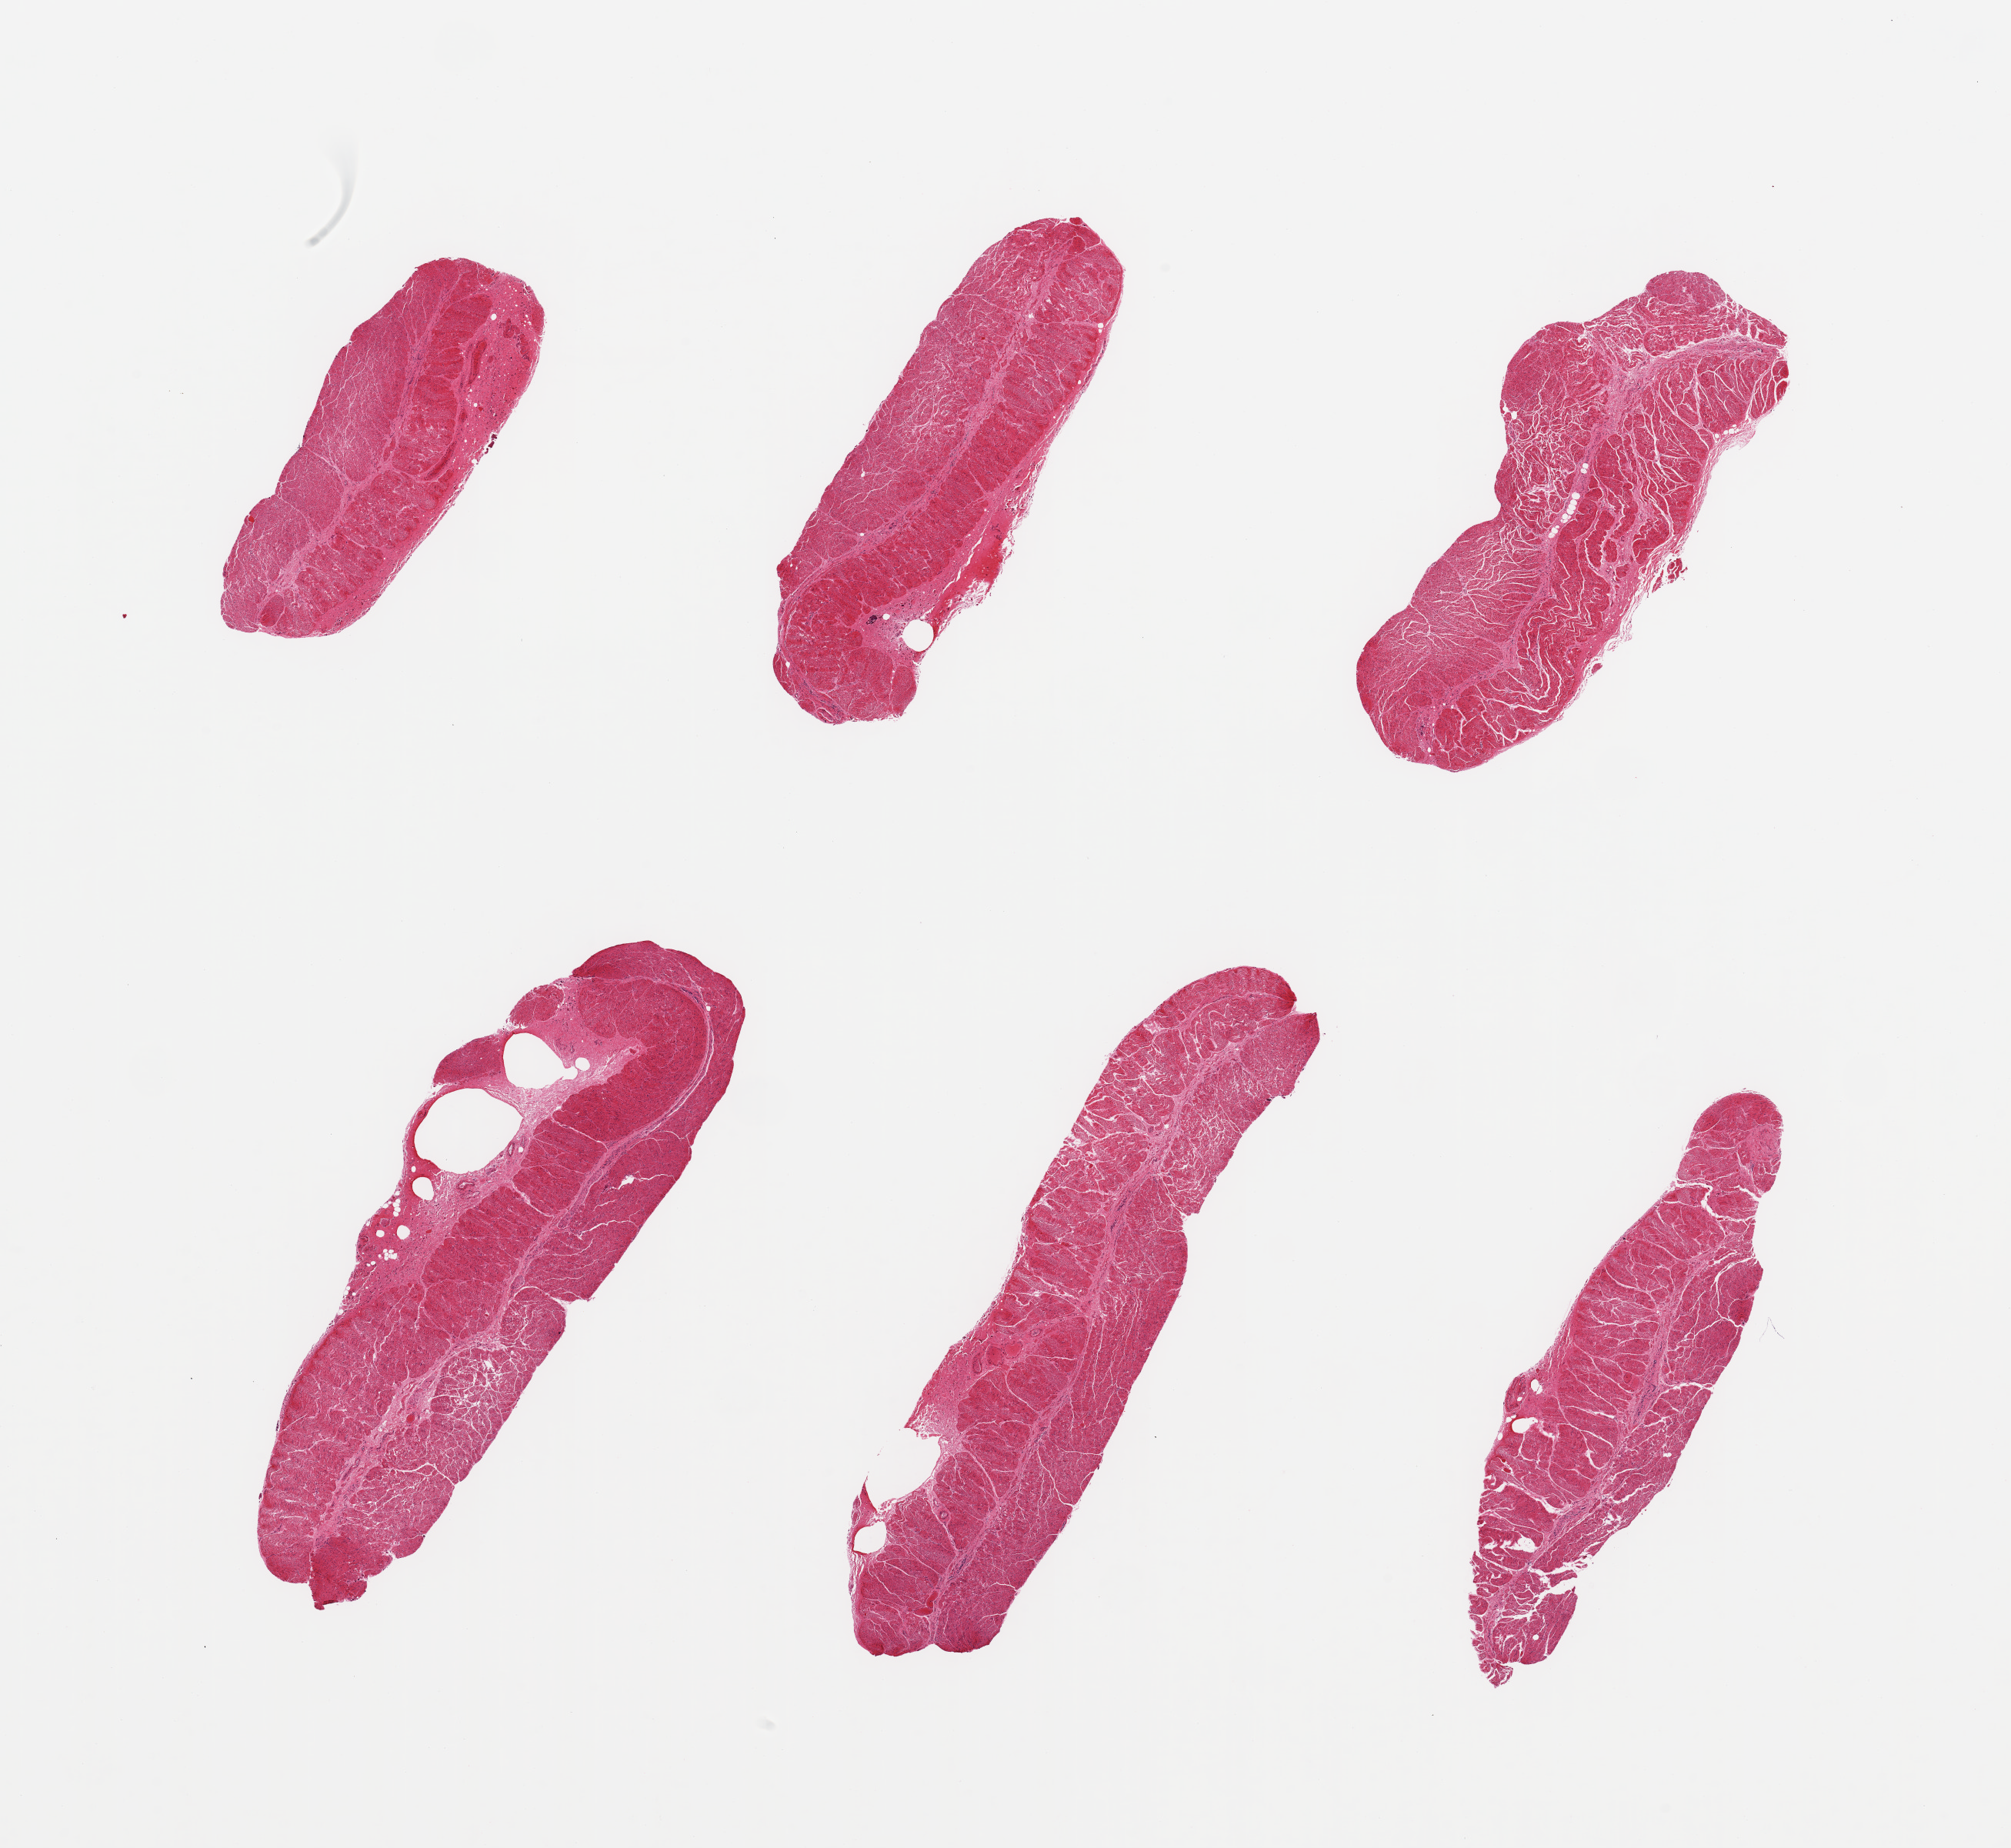
Whole-slide image, haematoxylin and eosin stain — shown as a low-resolution overview of the whole scanned area (about 20.7 x 19.0 mm, acquisition: 20x scan). PAXgene-fixed, paraffin-embedded tissue. Sampled site (target tissue): gastroesophageal junction. Tissue donor sample.
Pathologist's review note for this sample: 6 pieces, confirmed target muscularis.